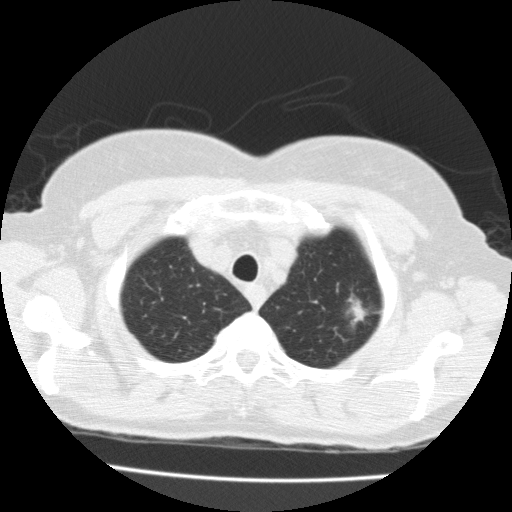
Low-dose screening chest CT, one axial slice; position 159 of 183 along the scan axis; reconstruction kernel FC10; 120 kVp; lung window (W 1500 / L -600 HU); 2 mm slice thickness; 512 × 512 image matrix, field of view 320 × 320 mm.
Outlined on this slice (manually delineated by an expert):
- lesion 1 (tumor, upper lobe of left lung): bounding box [x1, y1, x2, y2] px = [349, 298, 366, 324]